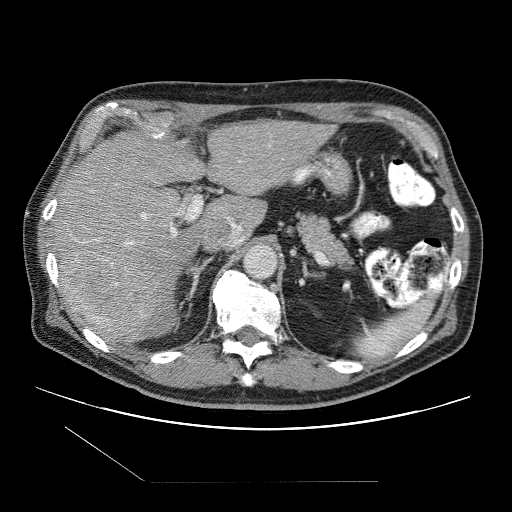
Contrast-enhanced abdominal CT (liver protocol), one axial slice; position 62 of 109 along the scan axis; one of 2 acquisitions stored at this slice position; soft-tissue window (W 400 / L 40 HU); 2.5 mm slice thickness; 512 × 512 image matrix, field of view 400 × 400 mm. From the clinical record (not read from this slice): diagnosis: hepatocellular carcinoma (patient treated with transarterial chemoembolisation; whether this scan precedes or follows treatment is not stated here); TNM stage (as recorded): Stage-IIIB; Child-Pugh class: A; tumour differentiation: well differentiated; tumour nodularity: multinodular.
Annotated regions visible in this slice (semi-automatic segmentation, software-assisted and operator-edited):
- liver parenchyma outside the tumour (the mass and vessels are separate outlines, so this box may not span the whole liver): bounding box (x1, y1, x2, y2) in pixels: (54, 120, 334, 340)
- mass: (61, 251, 156, 339)
- liver vessels: (75, 160, 242, 246)